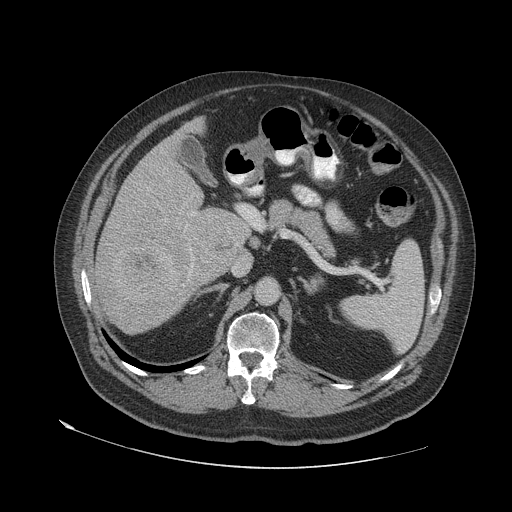
Contrast-enhanced abdominal CT (liver protocol), one axial slice; slice 33 of 79 in the series (ordered by position); 140 kVp; soft-tissue window (W 400 / L 40 HU); 2.5 mm slice thickness; 512 × 512 image matrix, field of view 480 × 480 mm. Case-level facts recorded for this patient, not image findings: diagnosis: hepatocellular carcinoma (patient treated with transarterial chemoembolisation; whether this scan precedes or follows treatment is not stated here); TNM stage (as recorded): Stage-IVA; Child-Pugh class: A; tumour differentiation: well differentiated.
Annotated regions visible in this slice (semi-automatic segmentation, software-assisted and operator-edited):
- liver parenchyma outside the tumour (the mass and vessels are separate outlines, so this box may not span the whole liver): bounding box [x1, y1, x2, y2] px = [92, 117, 250, 332]
- mass: [111, 239, 178, 301]
- liver vessels: [183, 226, 193, 286]